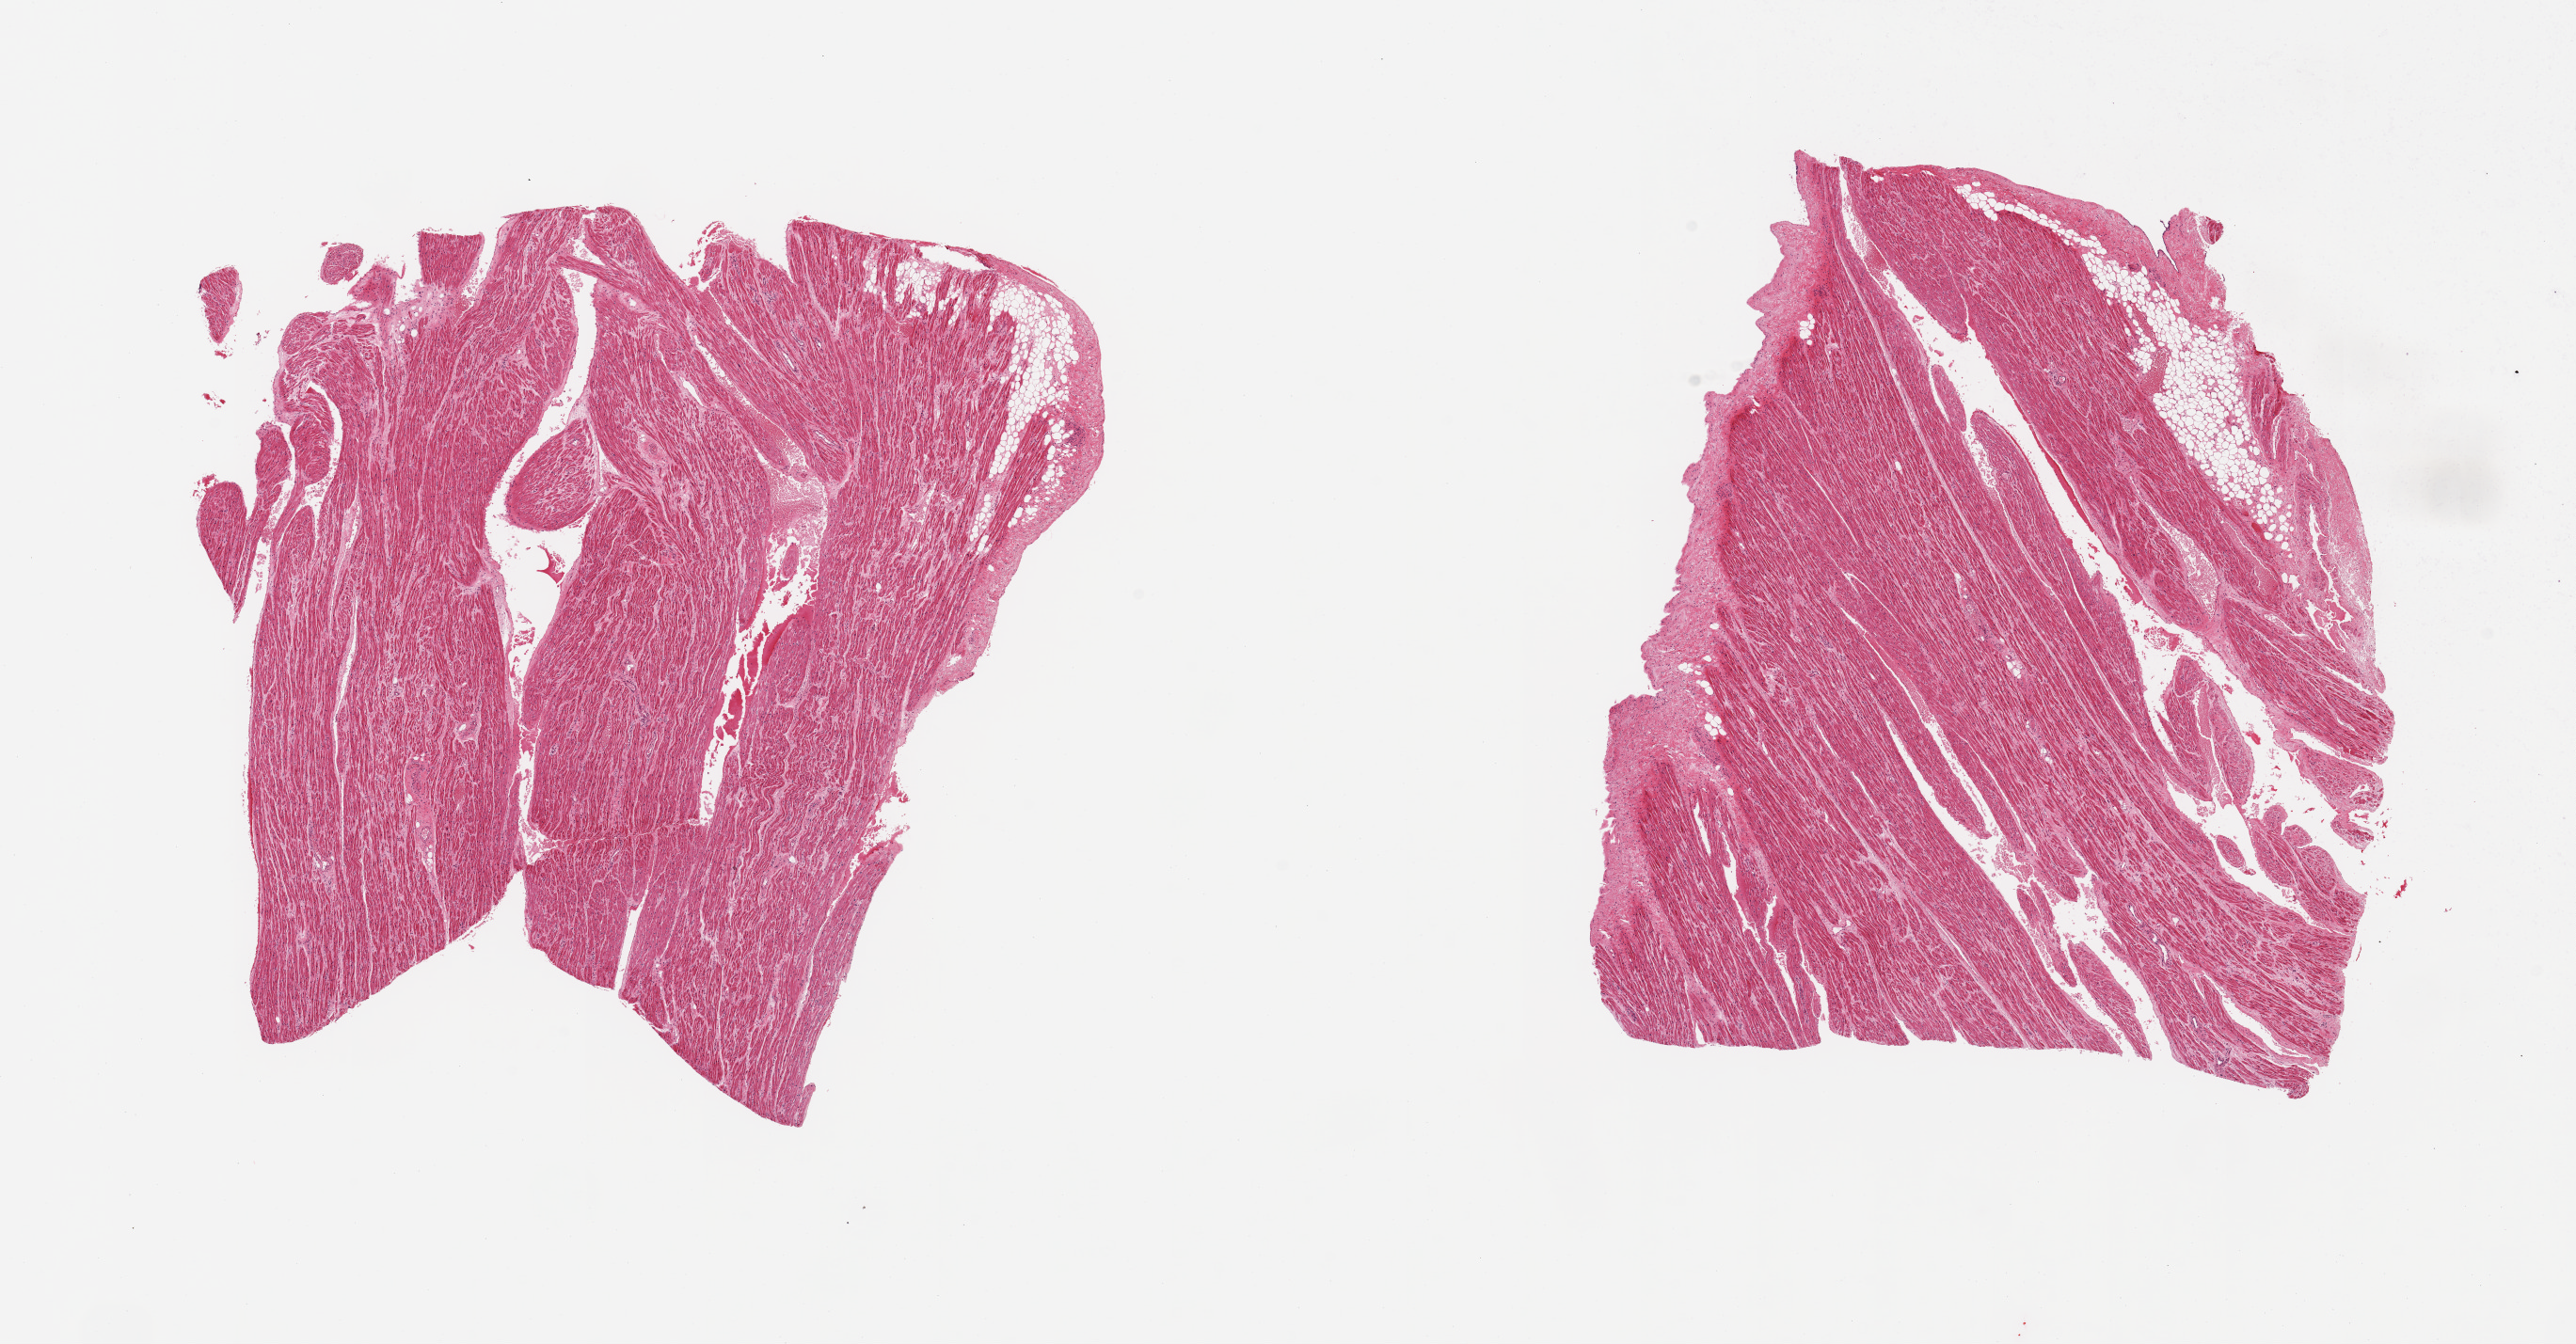
Hematoxylin and eosin (H&E) whole-slide image, whole scanned area (about 21.7 x 11.3 mm, slide scanned at 20x) shown as a low-resolution overview. PAXgene-fixed paraffin-embedded (PFPE) section. Sampled site (target tissue): auricular appendage. Tissue donor sample.
* review note (as recorded): 2 pieces; 1 piece has 10% fibrofatty content